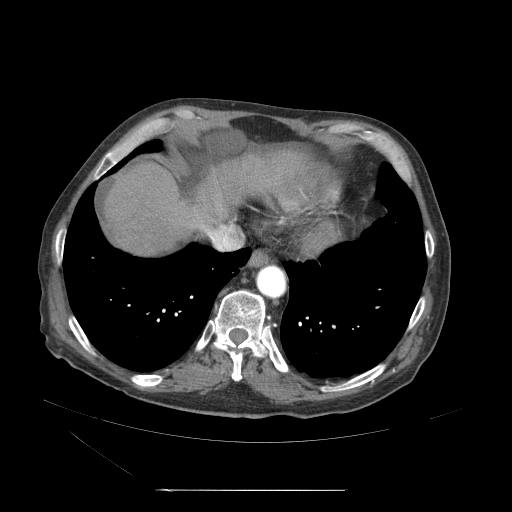
Contrast-enhanced abdominal CT (liver protocol), one axial slice. Slice 54 of 71 in the series (ordered by position). Reconstruction kernel STANDARD. 120 kVp. Soft-tissue window (W 400 / L 40 HU). 512 × 512 image matrix, field of view 440 × 440 mm. Case-level facts recorded for this patient, not image findings: diagnosis: hepatocellular carcinoma (patient treated with transarterial chemoembolisation; whether this scan precedes or follows treatment is not stated here); TNM stage (as recorded): Stage-II; Child-Pugh class: A; tumour size: 1 cm.
Annotated regions visible in this slice (semi-automatic segmentation, software-assisted and operator-edited):
- abdominal aorta: bounding box <257,266,287,299> (left, top, right, bottom; pixels)
- liver parenchyma outside the tumour (the mass and vessels are separate outlines, so this box may not span the whole liver): <119,148,321,252>
- liver vessels: <120,198,248,252>